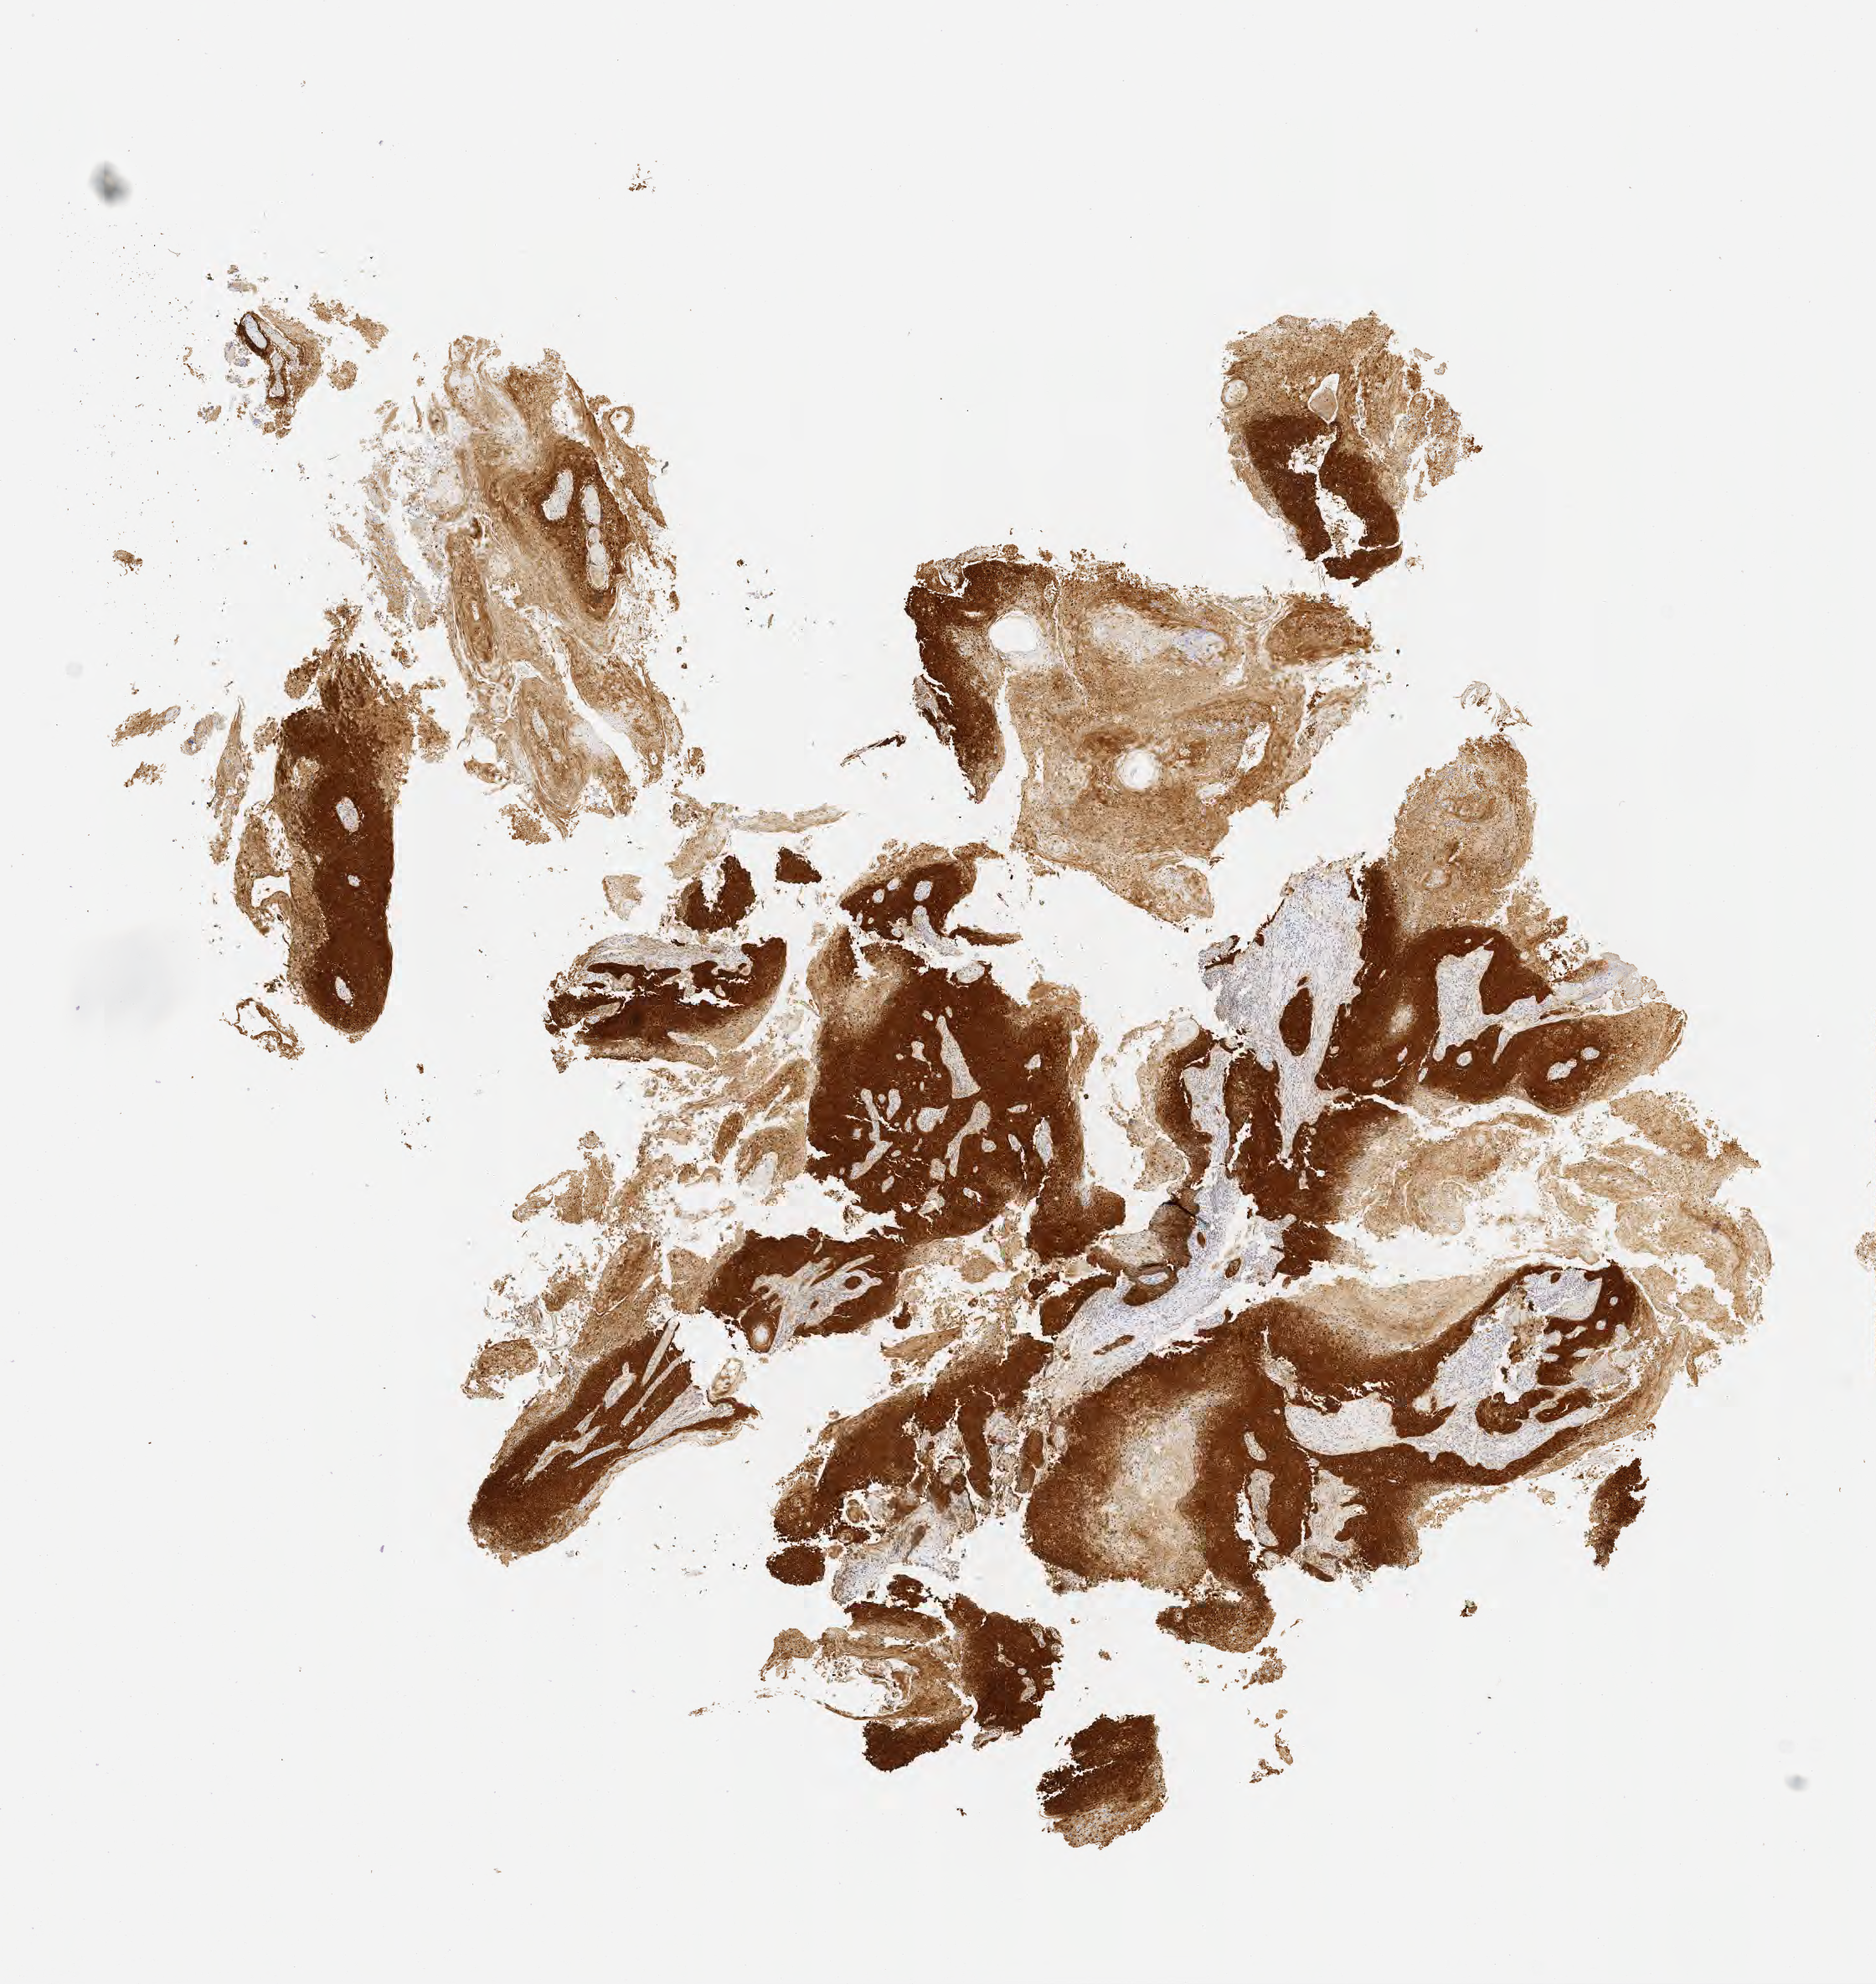
Immunohistochemistry (IHC) whole-slide image stained for p16 (p16INK4a), low-resolution overview of the scanned area, about 9.1 x 9.6 mm. Tumor tissue. Anatomic site: cervix. Female patient, aged 42.
* diagnosis: Squamous cell carcinoma, keratinizing, NOS